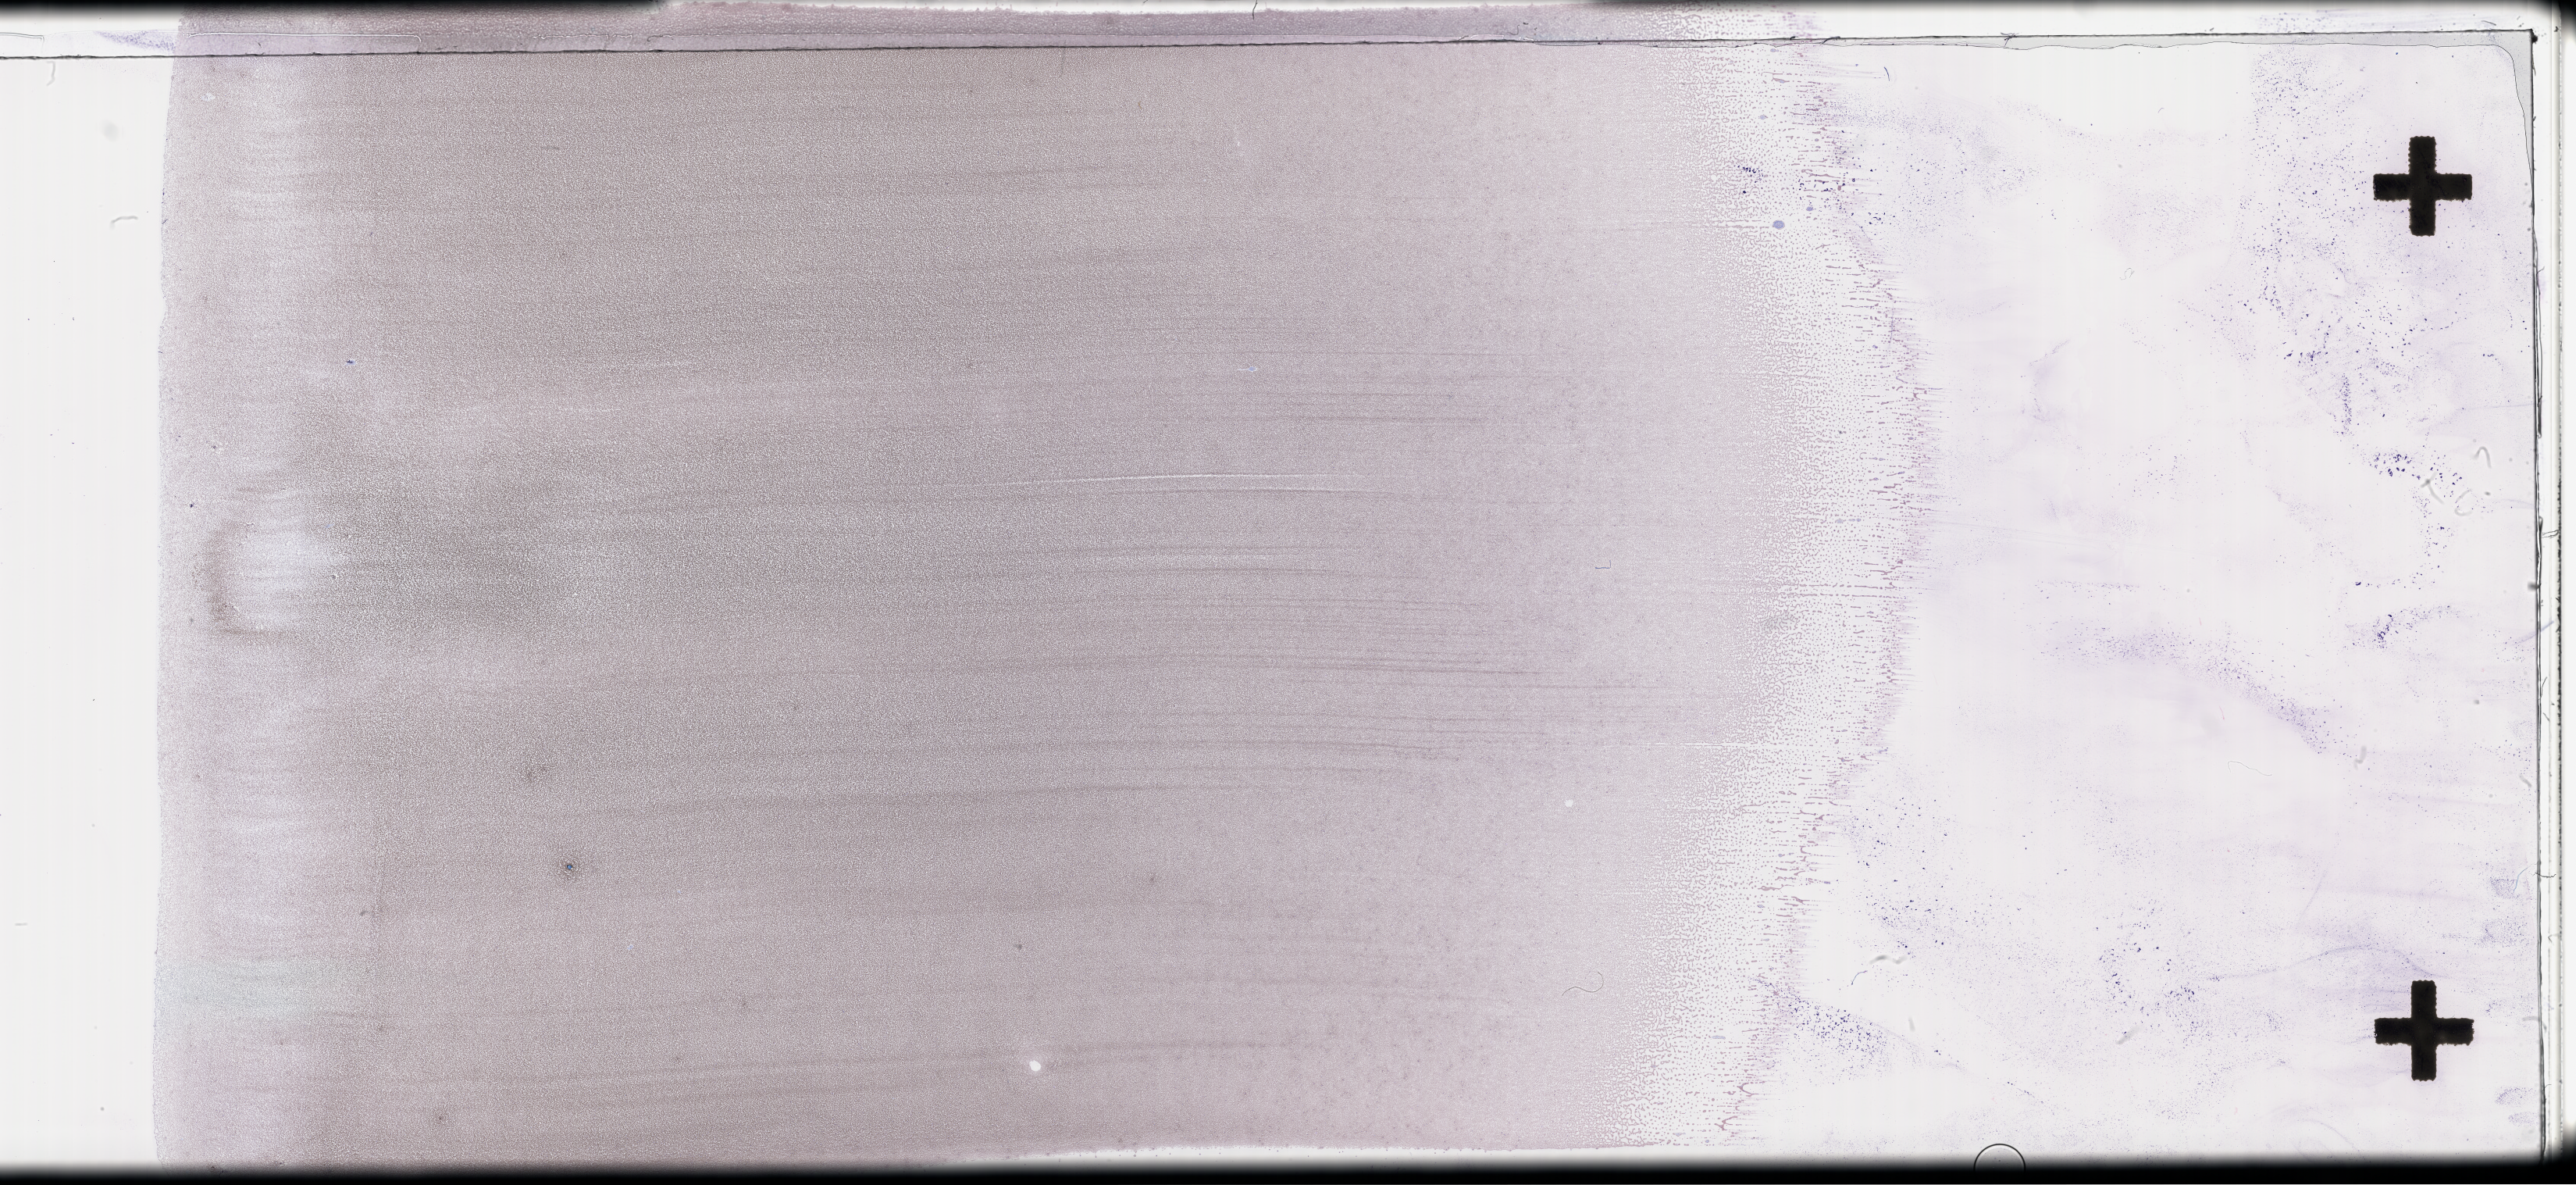
Wright–Giemsa-stained whole blood smear, whole-slide image — whole scanned area (about 53.3 x 24.5 mm) shown as a low-resolution overview. Female patient.
From a patient with: Plasma Cell Myeloma.